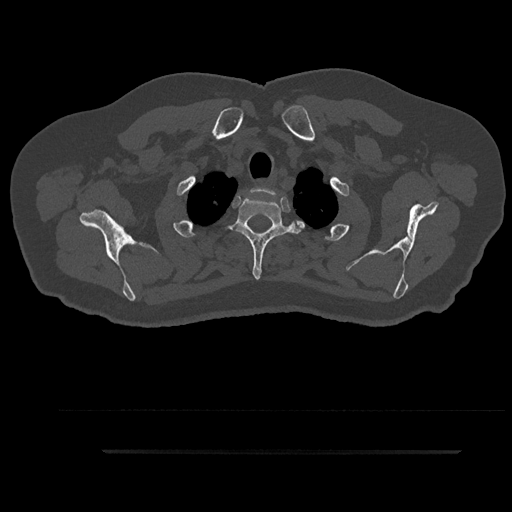
CT including the spine, one axial slice; position 758 of 797 along the scan axis; 120 kVp; bone window (W 1800 / L 400 HU); 0.5 mm slice thickness; 512 × 512 image matrix. Patient: male, 63 years. Case-level facts recorded for this patient, not image findings: primary cancer: renal; vertebrae with lytic lesions (as recorded): T8.
Structures marked on this image (semi-automatic segmentation, software-assisted and operator-edited):
- T1 vertebra: bounding box [x1, y1, x2, y2] px = [252, 187, 284, 209]
- T2 vertebra: [229, 197, 304, 280]
- T3 vertebra: [219, 245, 293, 248]